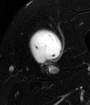
MRI of an extremity soft-tissue mass, one axial slice. Slice 45 of 65 in the series (ordered by position). T2-weighted fat-saturated. MR volume resampled by the dataset authors to the PET/CT grid (not the native acquisition matrix). 3.27 mm slice thickness. 90 × 105 image matrix. Male patient. From the clinical record (not read from this slice): histological type: mixoid liposarcoma; grade: low; site of the primary tumour: left thigh.
Outlined on this slice (expert contour drawn on MRI and transferred to this co-registered scan by the dataset authors):
- gross tumour volume (mass): box from (x=27, y=32) to (x=60, y=65) px